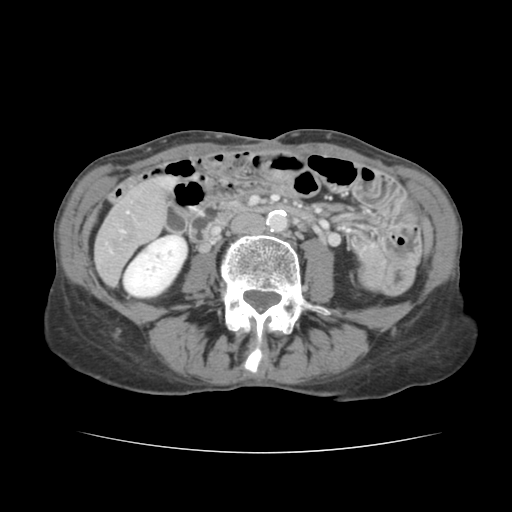
Contrast-enhanced abdominal CT, one axial slice; position 29 of 136 along the scan axis; 120 kVp; intravenous contrast given; soft-tissue window (W 400 / L 40 HU); 2.5 mm slice thickness; 512 × 512 image matrix. Female patient, age 77 years. From the clinical record (not read from this slice): diagnosis: colorectal cancer liver metastases, imaged before liver resection; multiple liver metastases: yes.
Annotated regions visible in this slice (outlined manually by an expert reader):
- liver: bounding box [x1, y1, x2, y2] px = [96, 179, 172, 283]